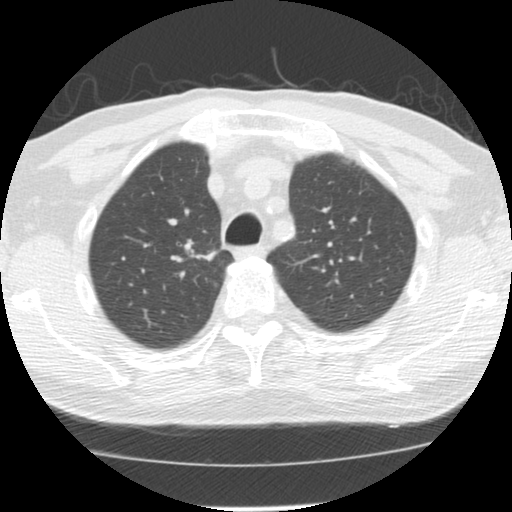
Chest CT (low-dose screening protocol), one axial image, first (baseline) screen, lung window (W 1500 / L -600 HU), 2.5 mm slice thickness, standard (soft-tissue) reconstruction kernel (STANDARD), 120 kVp, slice 35 of 139 in the series, 512 × 512 image matrix, field of view 310 × 310 mm. Male participant, aged 64 years at enrolment. Former smoker at enrolment.
• Expert-annotated lung lesion, bounding box <172,233,224,276> (left, top, right, bottom; pixels).
• Screening reader's record for this exam (one nodule recorded; not confirmed to be the boxed lesion): non-calcified nodule or mass ≥4 mm, right upper lobe, 20 × 13 mm, spiculated (stellate) margins, soft tissue attenuation.
• Official screen result: positive, change unspecified: nodule(s) >= 4 mm or enlarging nodule(s), mass(es), or other non-specific abnormalities suspicious for lung cancer.
• Lung cancer was diagnosed 73 days after this screen: adenocarcinoma, NOS, right upper lobe, moderately differentiated (G2), stage IA (AJCC 6th edition), 17 mm at pathology.